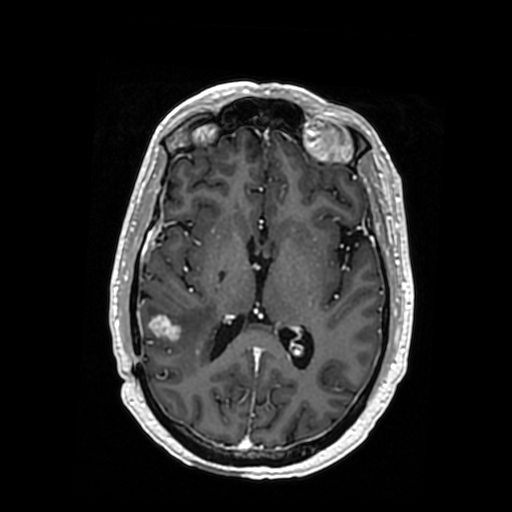
Brain MRI from a brain-tumour surgery series, one axial slice. Position 178 of 364 along the scan axis. T1-weighted post-contrast. 0.5 mm slice thickness. 512 × 512 image matrix, field of view 260 × 260 mm. From the clinical record (not read from this slice): histopathology: Oligodendroglioma; WHO grade: 3; IDH mutation: yes; tumour location: Right Posterior Temporal Inferior Parietal.
Structures marked on this image (manually delineated by an expert):
- tumour: bounding box [x1, y1, x2, y2] px = [151, 315, 207, 372]